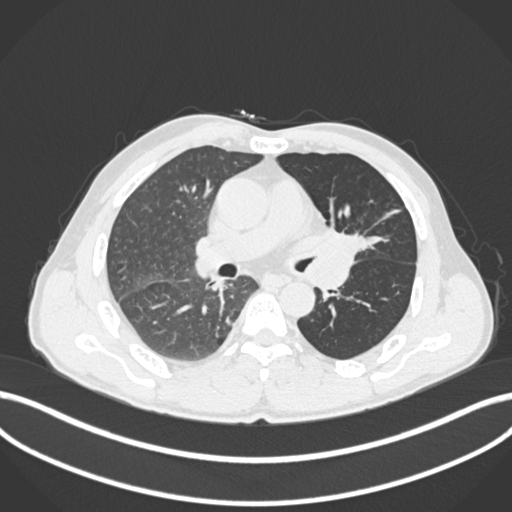
Chest CT, one axial slice. Position 106 of 255 along the scan axis. Reconstruction kernel B30f. 120 kVp. Lung window (W 1500 / L -600 HU). 1 mm slice thickness. 512 × 512 image matrix, field of view 400 × 400 mm. Male patient, age 57 years. Case-level facts recorded for this patient, not image findings: clinical TNM (as recorded): T2b N0 M0.
Structures marked on this image (rectangle marked by the reading radiologist):
- lung tumour (recorded histology: squamous cell carcinoma): bounding box (x1, y1, x2, y2) in pixels: (313, 224, 373, 262)